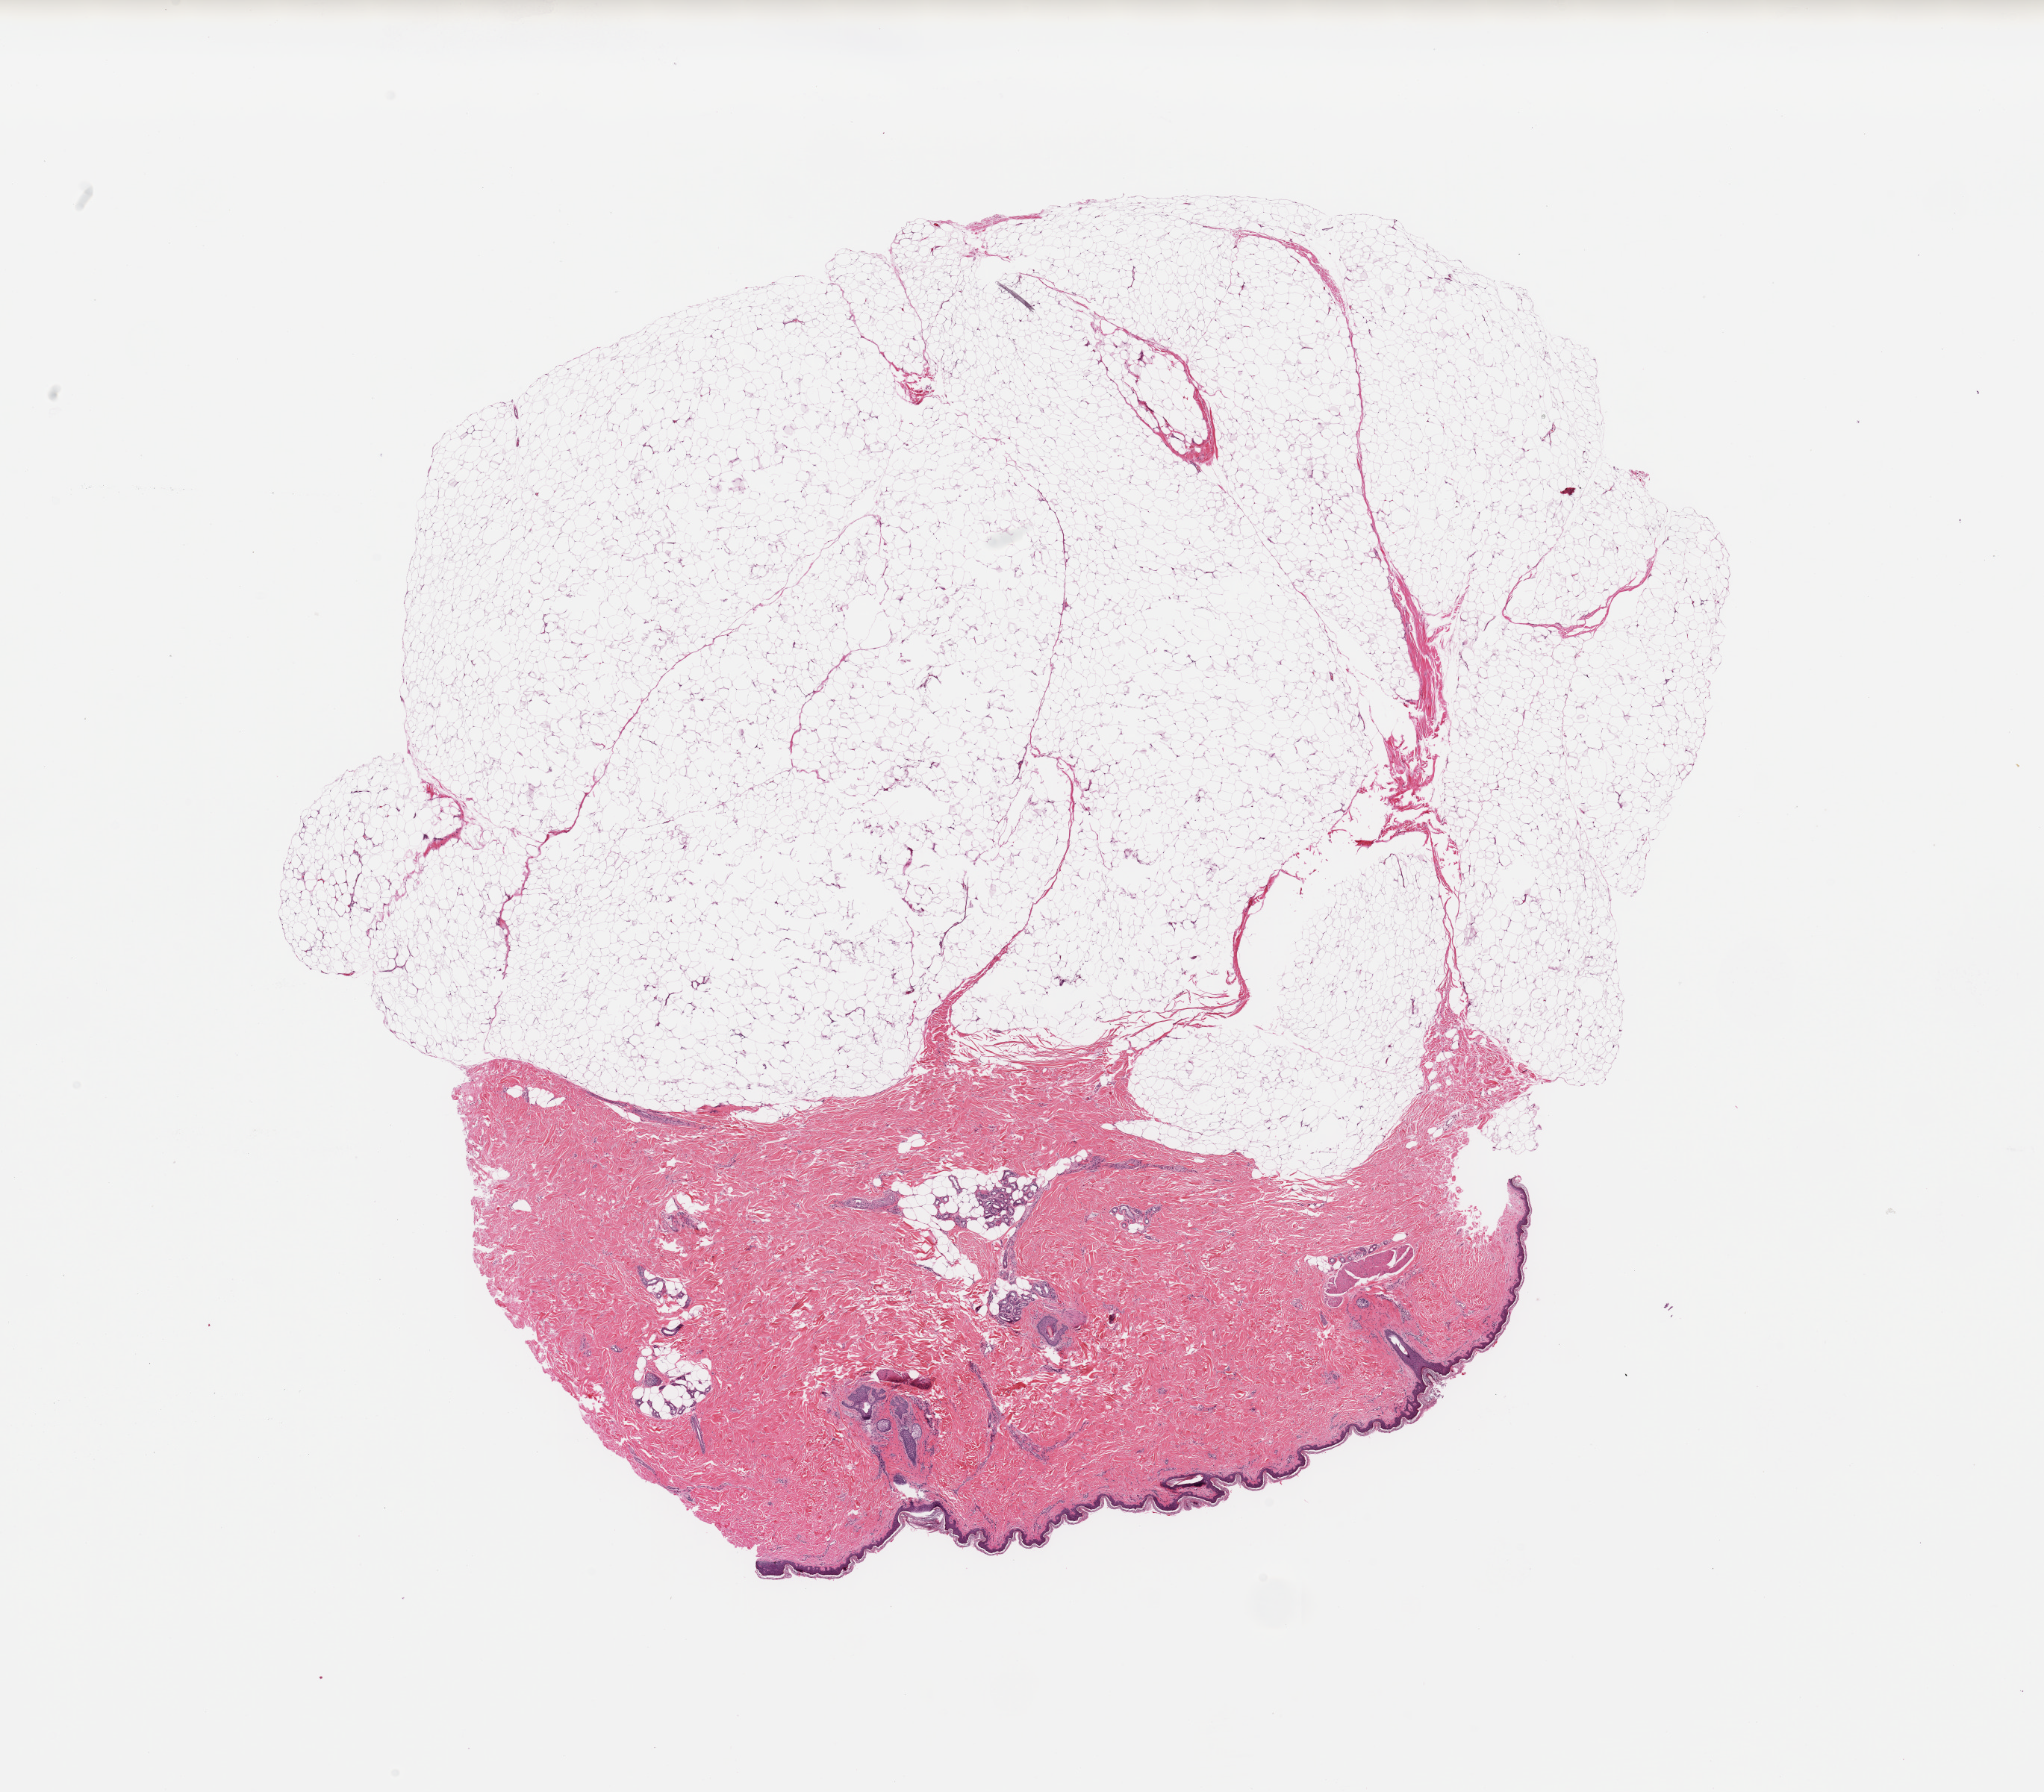
H&E-stained whole-slide image, a low-resolution overview of the entire scanned area, about 21.7 x 19.0 mm. Normal (non-tumour) tissue (melanoma cohort); sampled site not recorded. Patient: female, age 69 years.
- this section: normal (non-tumour) tissue from the same patient
- patient diagnosis: Malignant melanoma, NOS